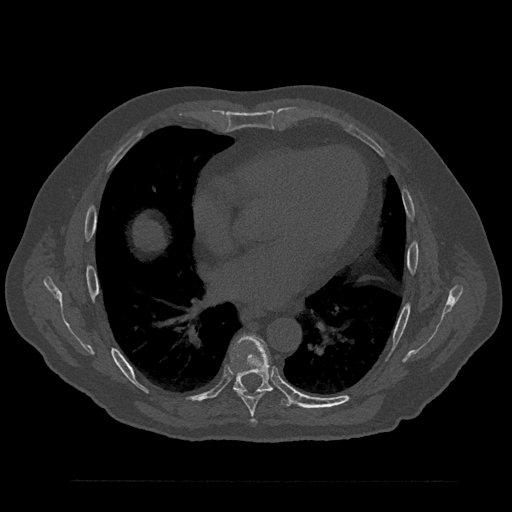
CT including the spine, one axial slice; position 482 of 797 along the scan axis; 120 kVp; bone window (W 1800 / L 400 HU); 0.5 mm slice thickness; 512 × 512 image matrix, field of view 430 × 430 mm. Male patient, age 61 years. Case-level facts recorded for this patient, not image findings: primary cancer: prostate.
Outlined on this slice (semi-automatically segmented with operator editing):
- T7 vertebra: bounding box (x1, y1, x2, y2) in pixels: (232, 359, 263, 424)
- T8 vertebra: (232, 335, 294, 406)